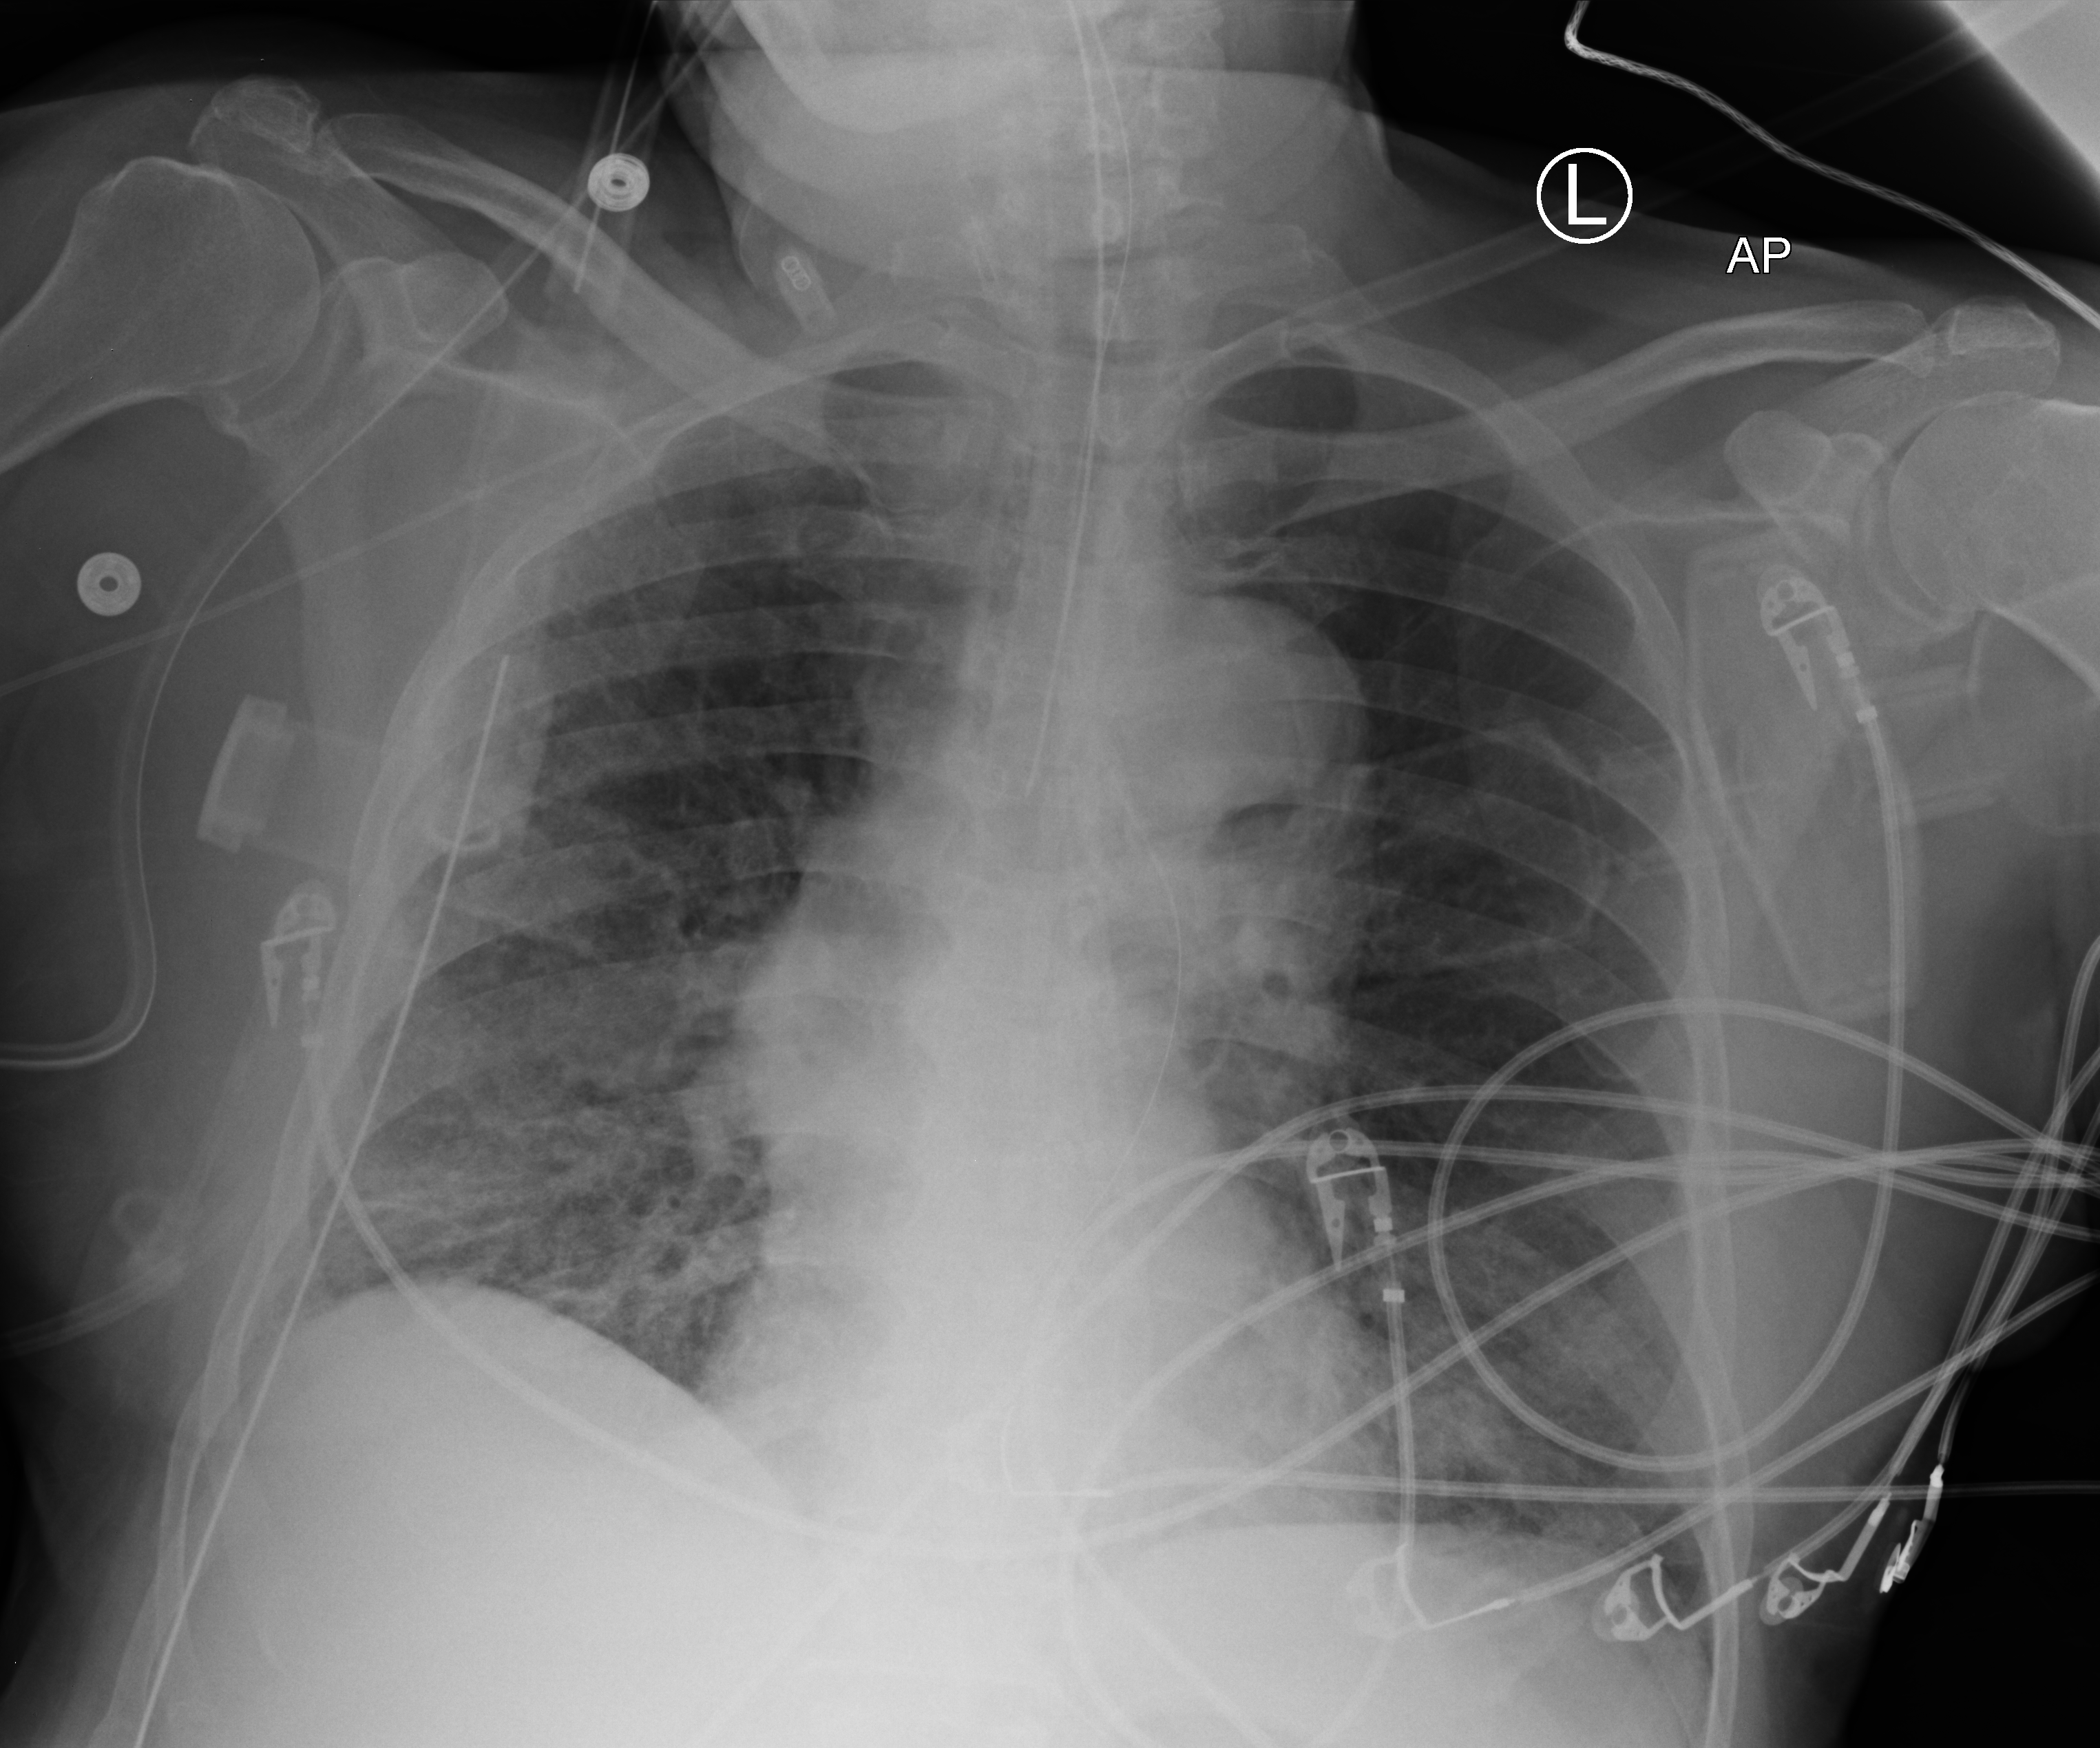
Chest X-ray (portable); anteroposterior (AP) projection. Male patient hospitalised with COVID-19, age 60–74 years.
Hospital-stay facts (about this admission, not read from this image; timing relative to this image not recorded):
- mechanically ventilated during this hospital stay: yes
- hypertension (admission record): yes